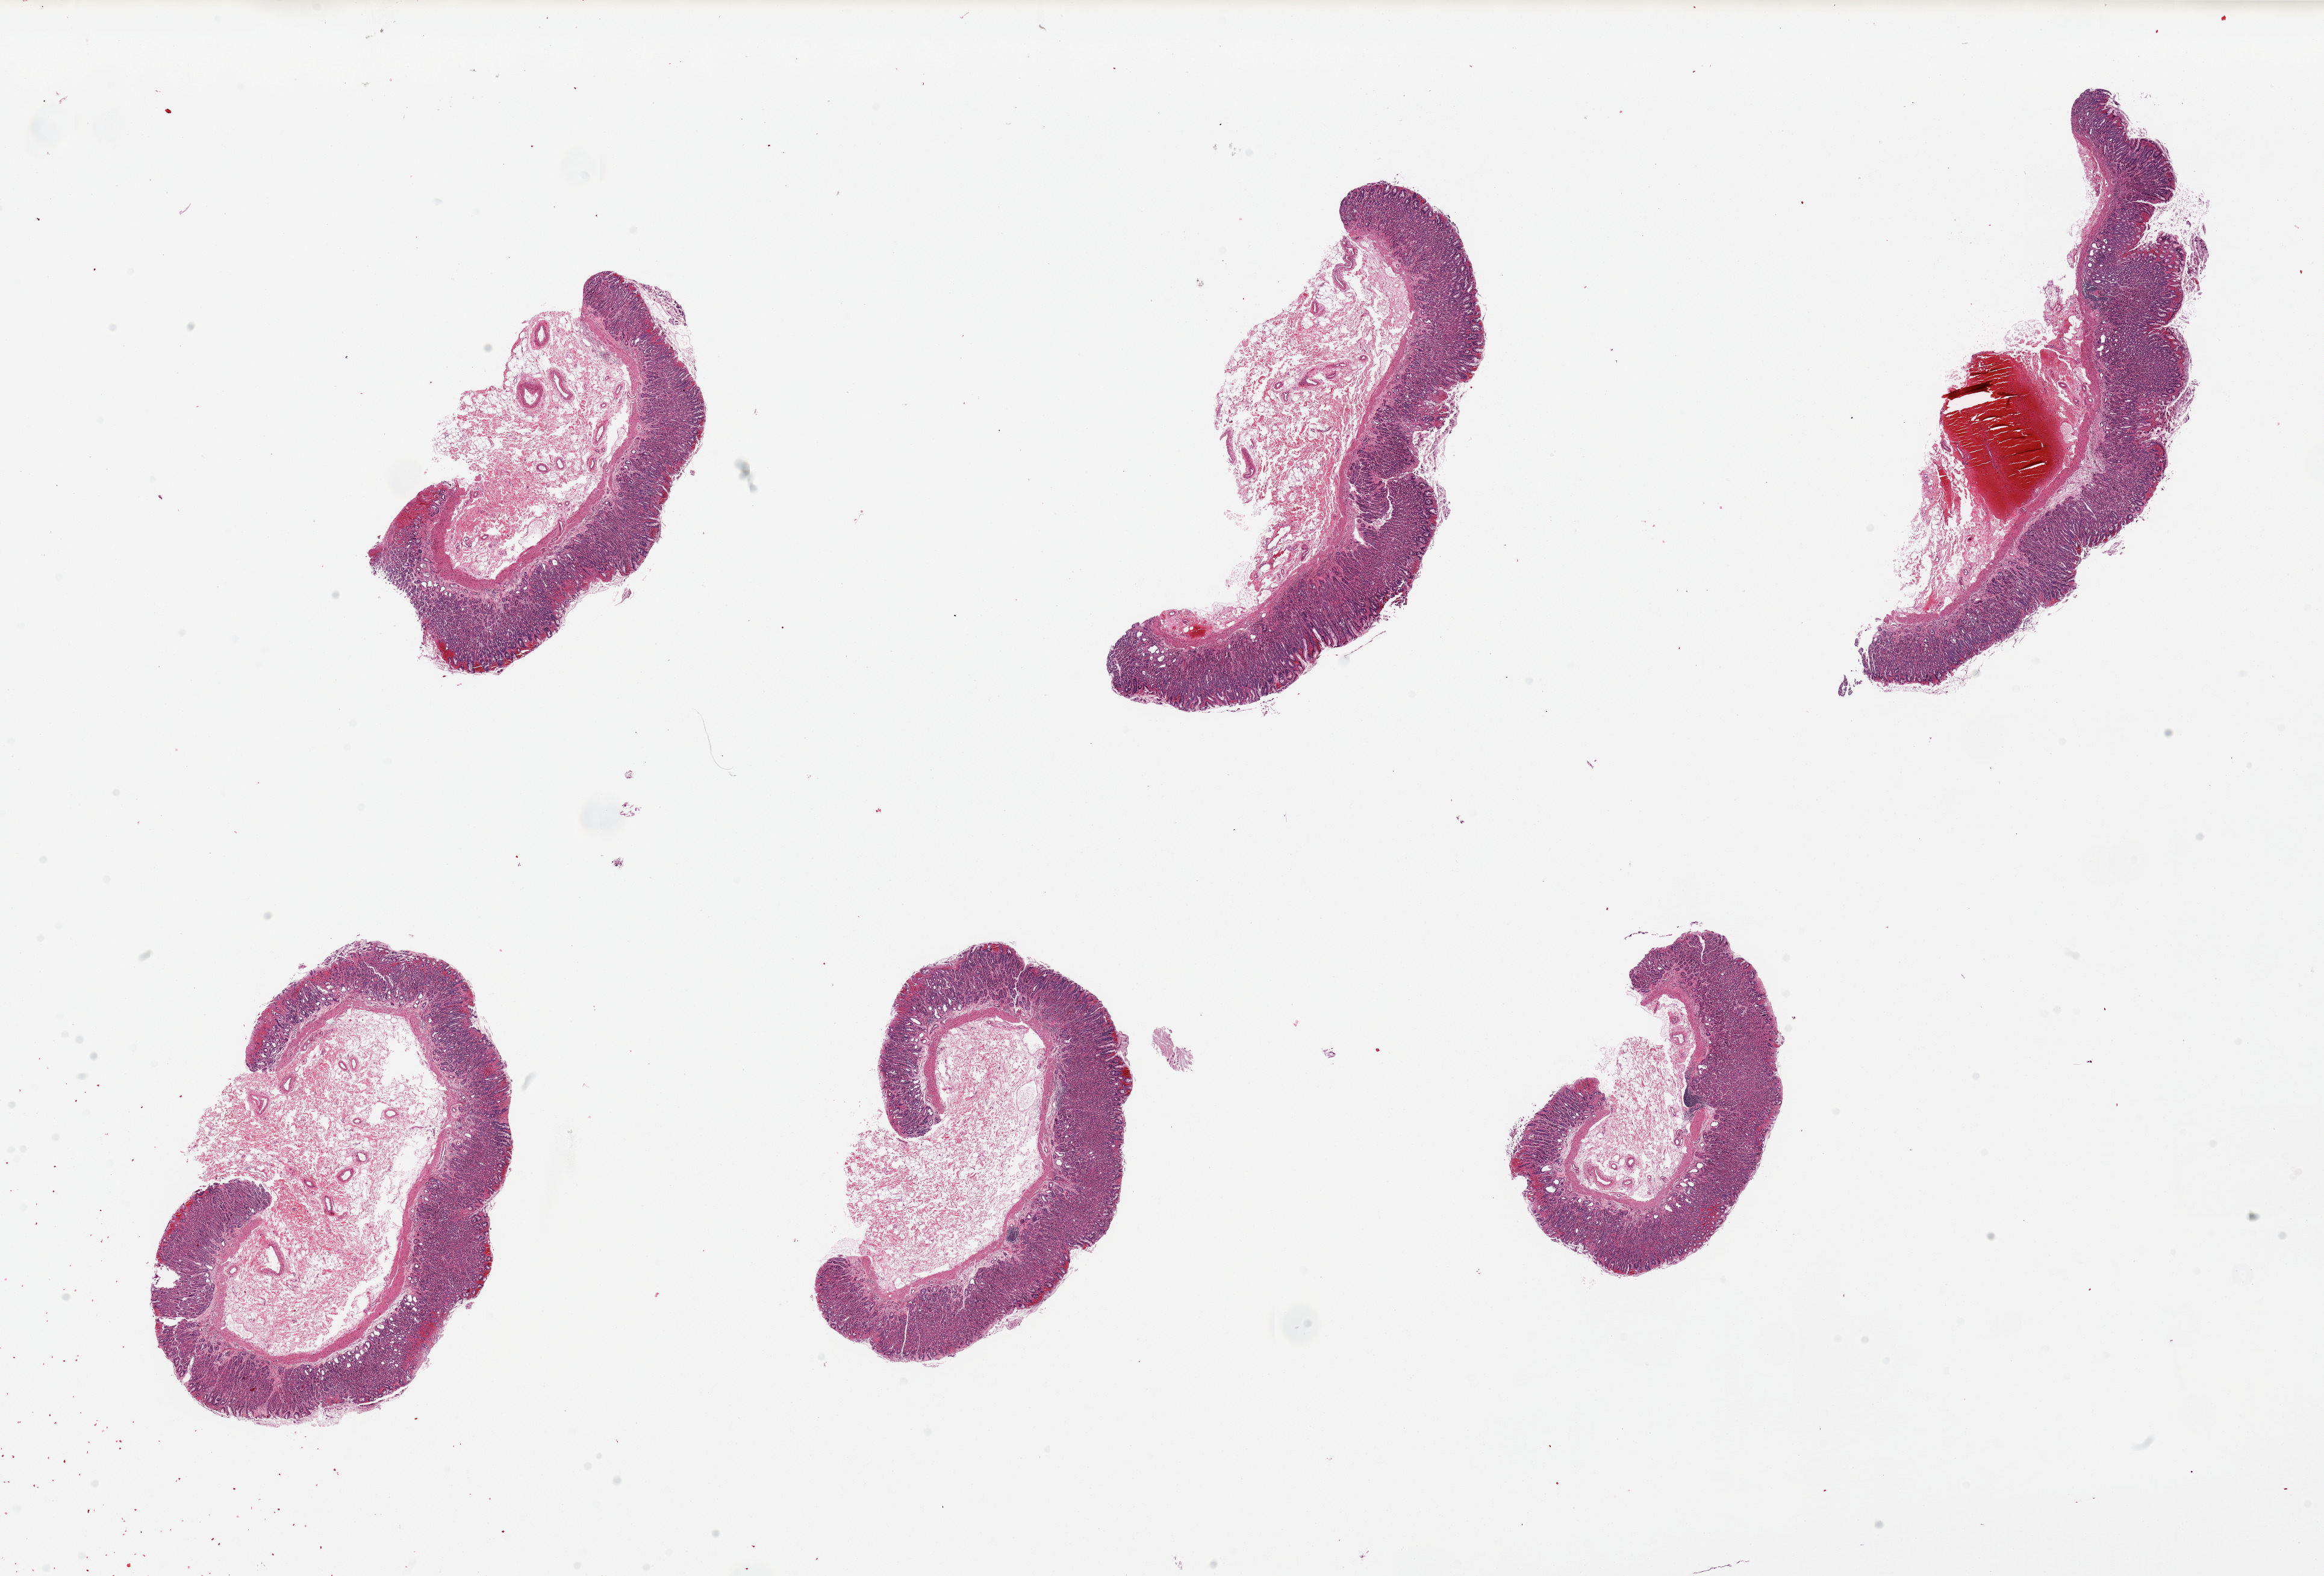
Digitized H&E-stained section — shown as a low-resolution overview of the whole scanned area (about 30.5 x 20.7 mm, acquisition: 20x scan); PAXgene-fixed, paraffin-embedded tissue; sampled site (target tissue): stomach; tissue donor sample.
Reviewer comment on this tissue sample: 6 pieces, up to 9x4mm; well - preserved mucosa ~30-70% thickness.